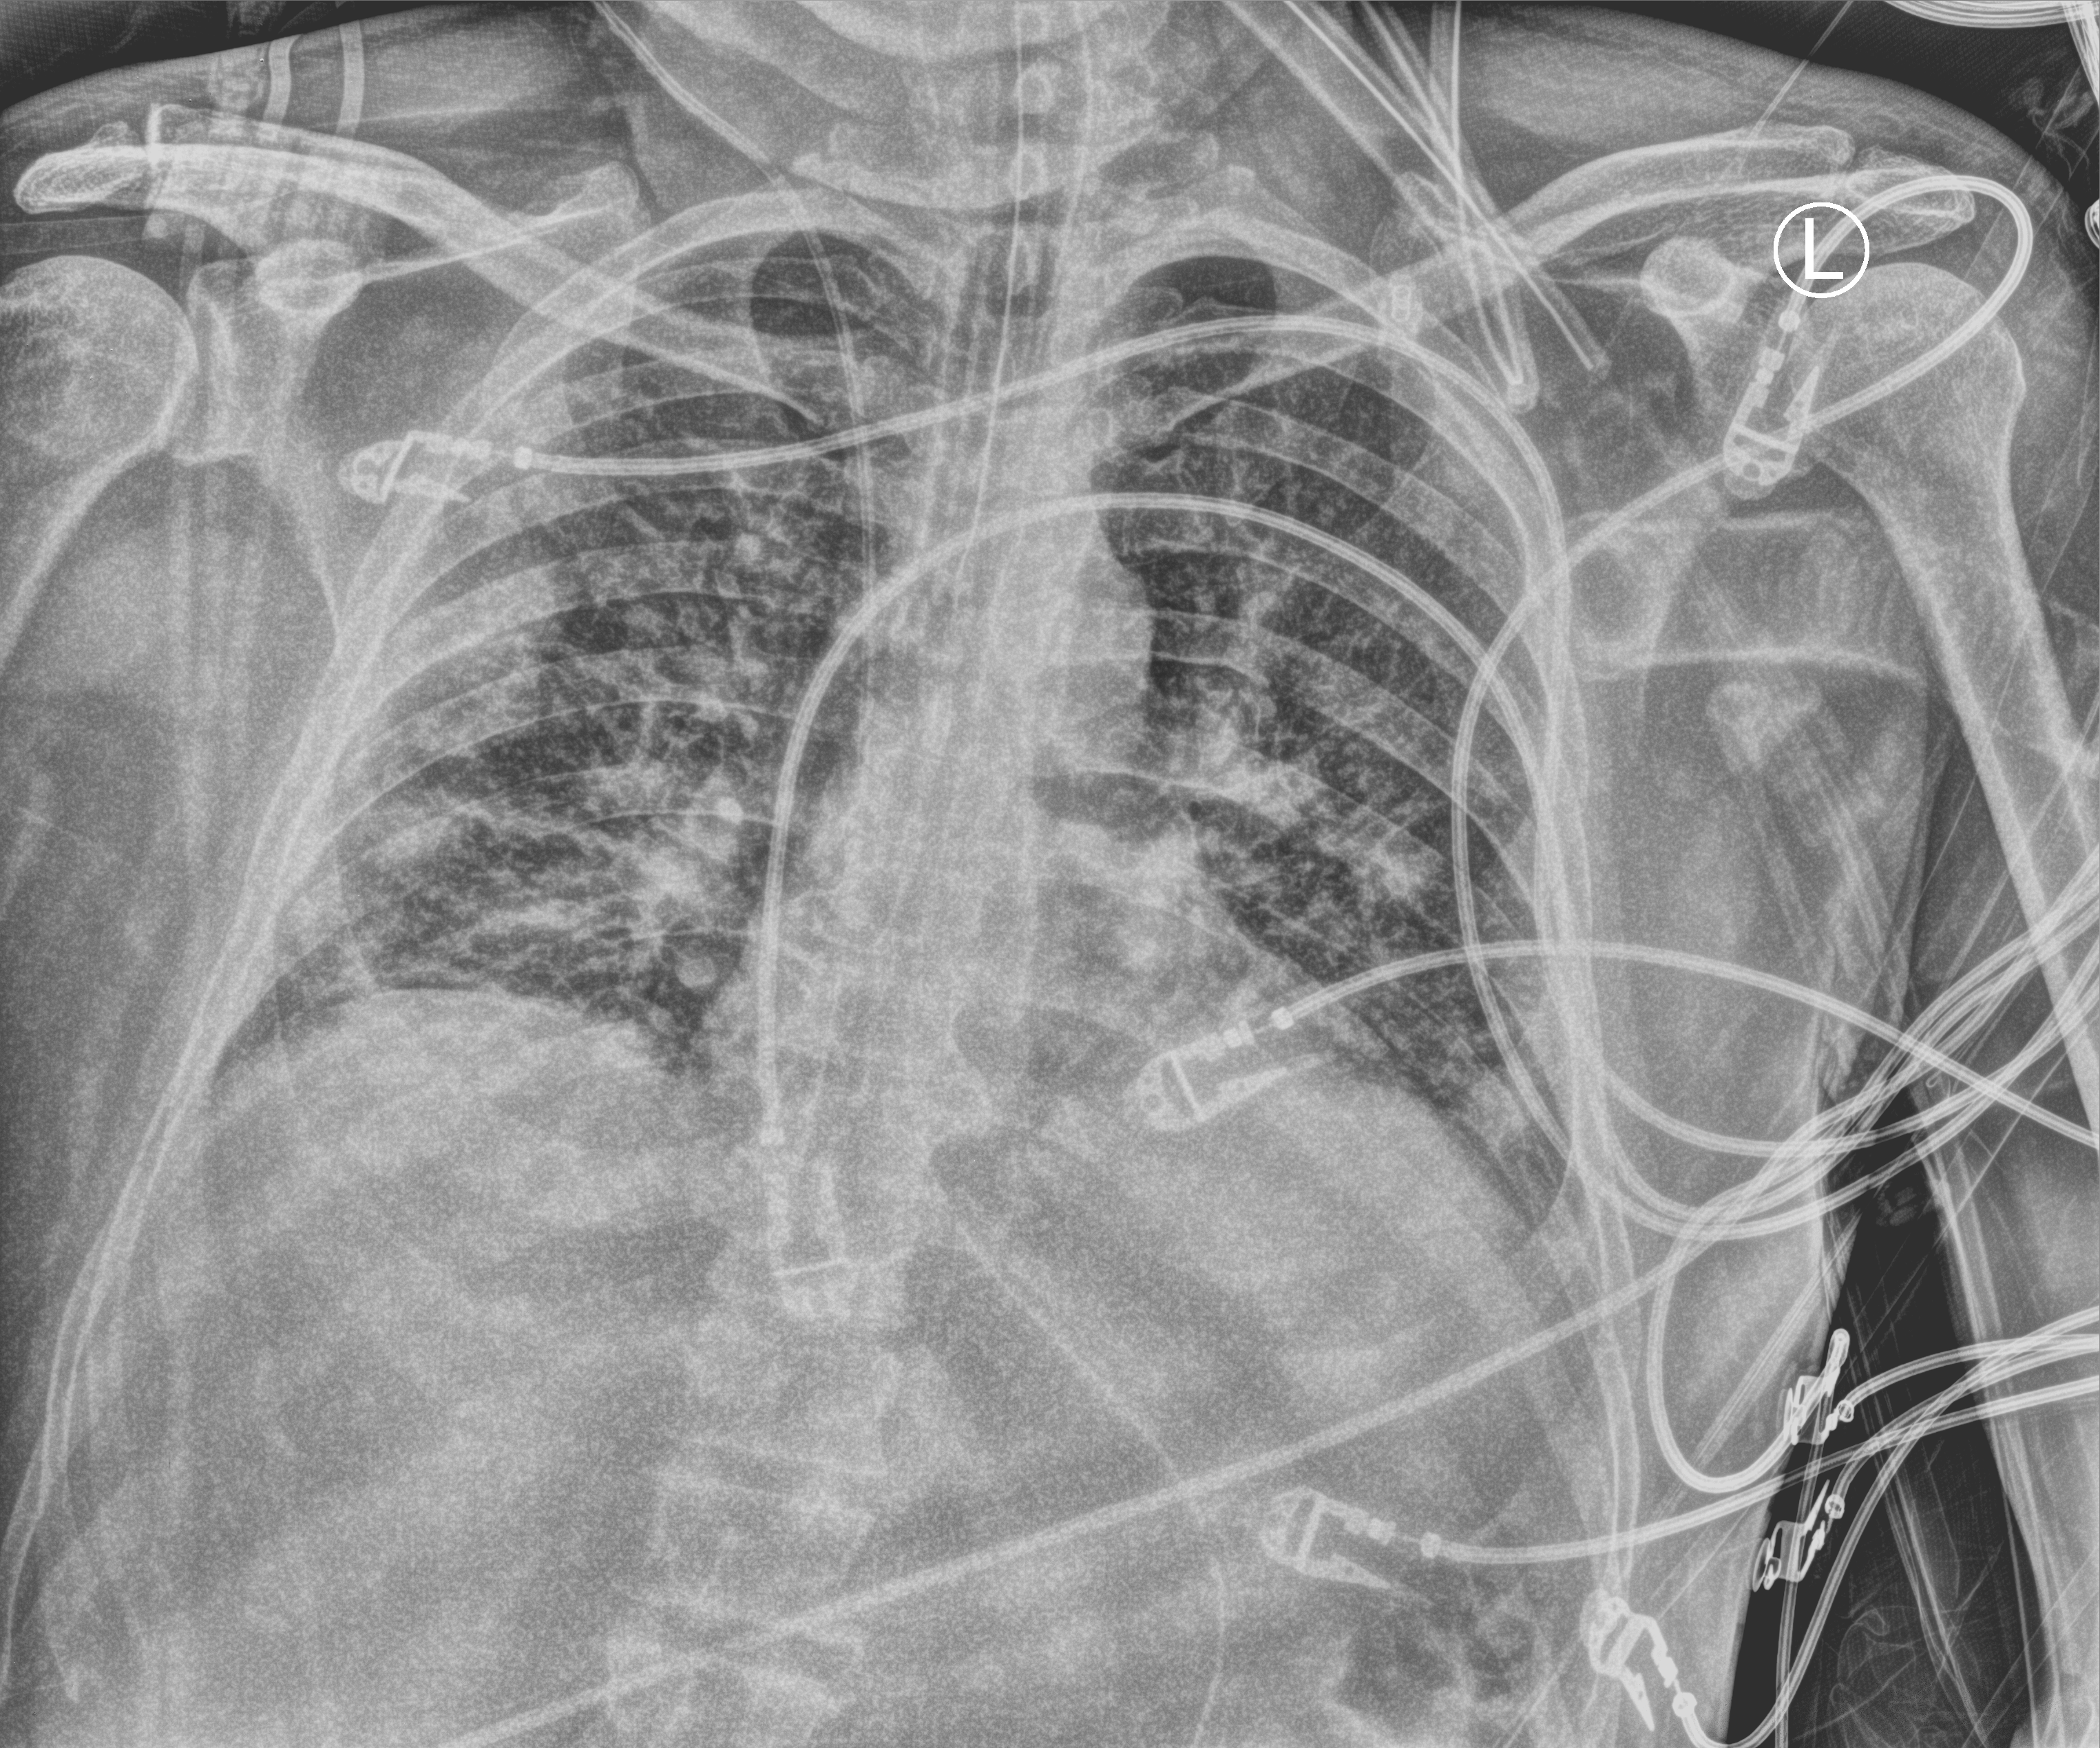
Portable chest radiograph. Patient hospitalised with COVID-19; male, aged 18–59 years.
Hospital-stay facts (about this admission, not read from this image; timing relative to this image not recorded):
- other chronic lung disease (admission record): no
- smoking status (admission record): former